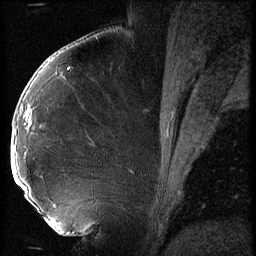
Breast MRI (dynamic contrast-enhanced), one sagittal slice; slice 30 of 56 in the series (ordered by position); 3 images stored at this slice position (order not interpretable as contrast timing); 1.5 T; TE 4.2 ms, TR 9 ms; 2.5 mm slice thickness; 256 × 256 image matrix, field of view 180 × 180 mm. Female patient, age 43 years. Case-level facts recorded for this patient, not image findings: setting: breast cancer imaged before/during neoadjuvant chemotherapy; receptor status: HER2-positive.
Outlined on this slice (semi-automatic segmentation, software-assisted and operator-edited):
- analysis volume of interest (the breast-tissue region the enhancement analysis was run in; not a lesion): bounding box <12,92,74,211> (left, top, right, bottom; pixels)
- tumour enhancement mask (voxels above the 140 % enhancement threshold inside the analysis volume of interest): <12,109,30,190>